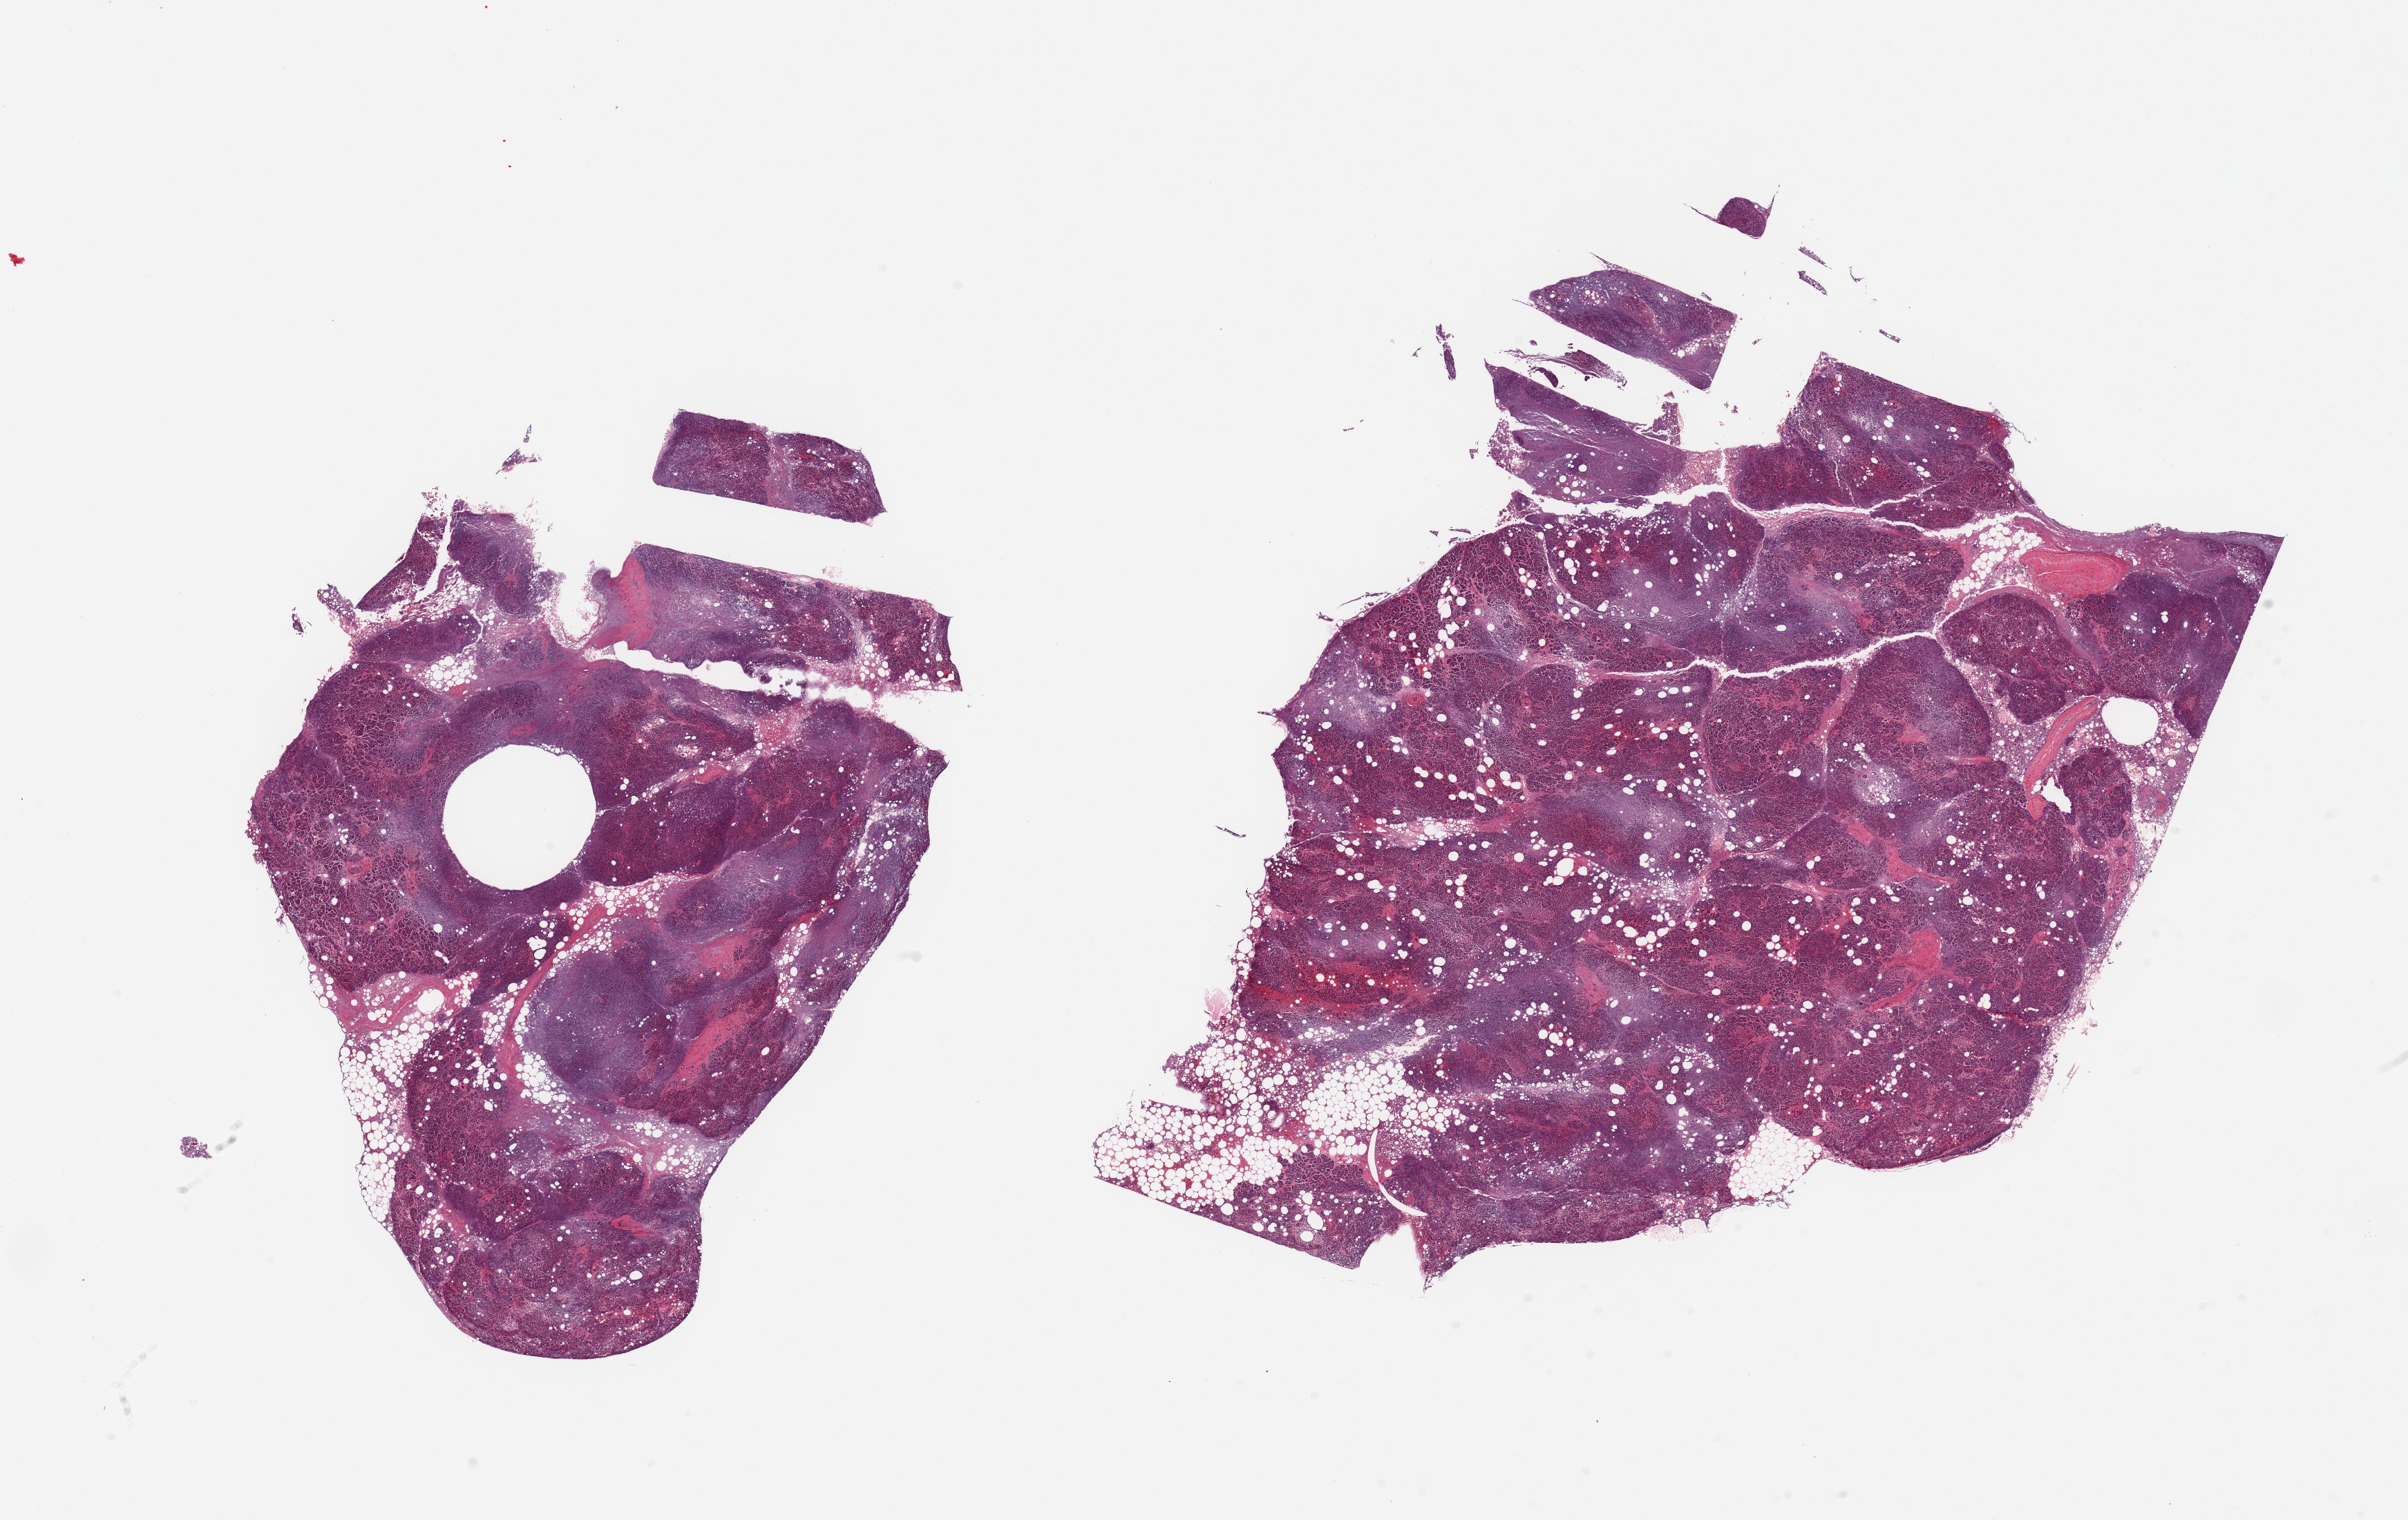
Digitized haematoxylin and eosin-stained section — low-resolution overview of the scanned area, about 27.6 x 17.4 mm (slide scanned at 20x); PAXgene-fixed, paraffin-embedded tissue; sampled site (target tissue): pancreas; donor tissue sample. Male donor.
- reviewer comment on this tissue sample: 2 pieces; 10% internal fat; islets not defined